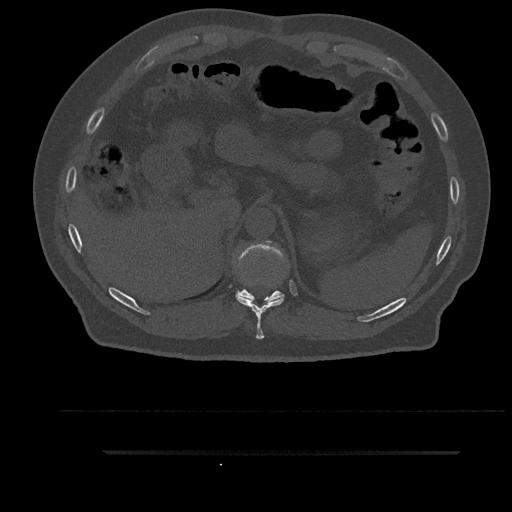
CT including the spine, one axial slice; position 337 of 797 along the scan axis; reconstruction kernel Br40s/3; bone window (W 1800 / L 400 HU); 0.5 mm slice thickness; 512 × 512 image matrix, field of view 432 × 432 mm. Male patient, age 63 years. Case-level facts recorded for this patient, not image findings: primary cancer: renal.
Annotated regions visible in this slice (semi-automatic segmentation, software-assisted and operator-edited):
- T10 vertebra: bounding box (x1, y1, x2, y2) in pixels: (236, 296, 284, 339)
- T11 vertebra: (236, 241, 284, 304)